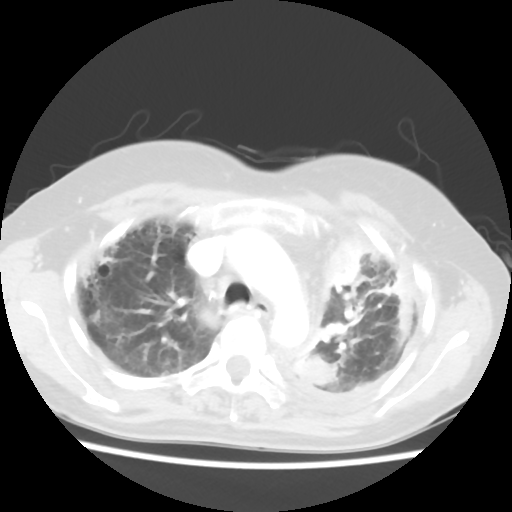
Chest CT, one axial slice. Slice 41 of 56 in the series (ordered by position). Reconstruction kernel STANDARD. 120 kVp. Lung window (W 1500 / L -600 HU). 5 mm slice thickness. 512 × 512 image matrix, field of view 309 × 309 mm. Patient: female, 56 years. From the clinical record (not read from this slice): clinical TNM (as recorded): T1c N0 M1.
Annotated regions visible in this slice (rectangle marked by the reading radiologist):
- lung tumour (recorded histology: adenocarcinoma): box from (x=319, y=227) to (x=365, y=291) px